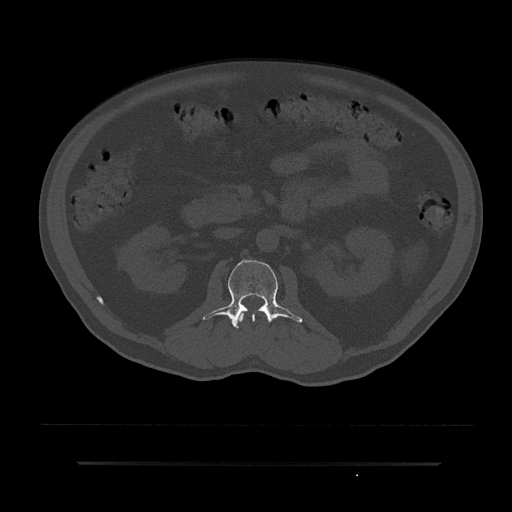
CT including the spine, one axial slice. Slice 85 of 797 in the series (ordered by position). Bone window (W 1800 / L 400 HU). 0.5 mm slice thickness. 512 × 512 image matrix. Patient: male, 59 years. Case-level facts recorded for this patient, not image findings: primary cancer: bile ducts; vertebrae with lytic lesions (as recorded): T10.
Annotated regions visible in this slice (semi-automatic segmentation, software-assisted and operator-edited):
- L1 vertebra: box from (x=236, y=311) to (x=265, y=325) px
- L2 vertebra: (x=202, y=260)–(x=303, y=328)